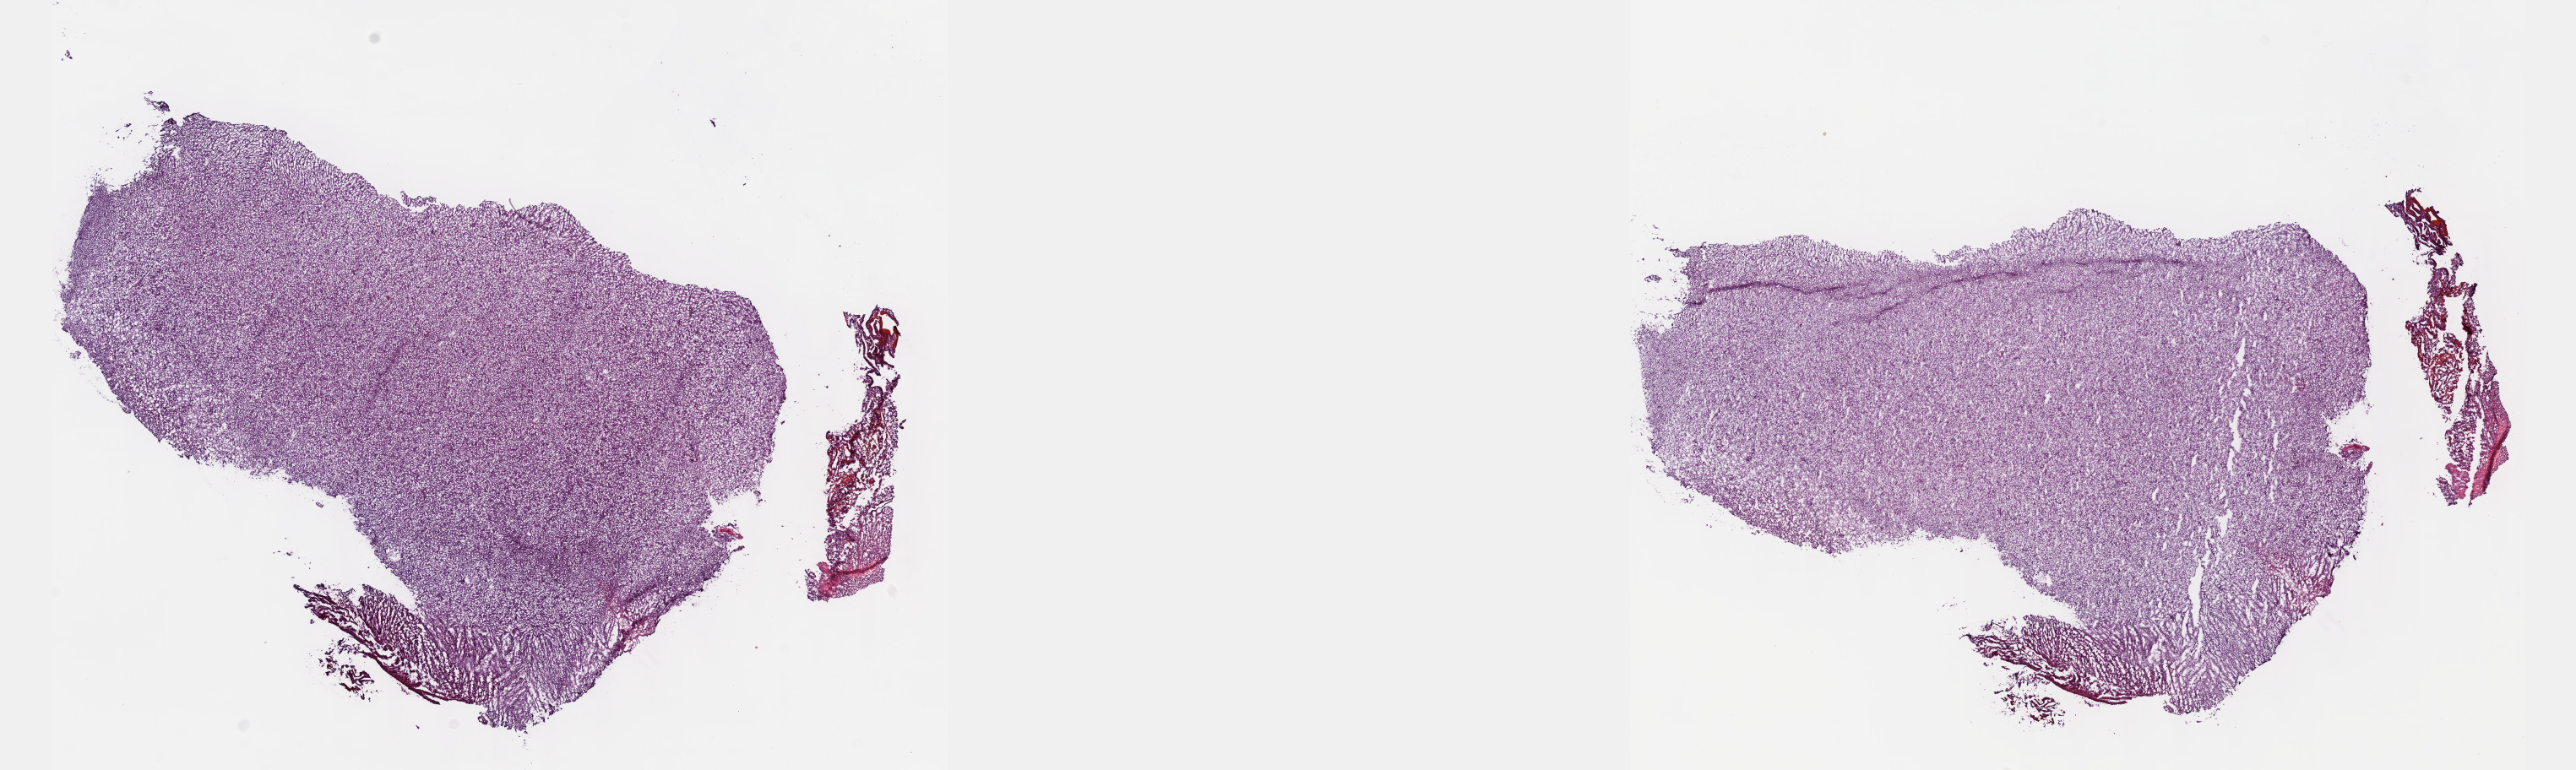
Whole-slide histology image, H&E, a low-resolution overview of the entire scanned area, about 24.6 x 7.4 mm (from a 40x scan). Frozen section. Sample: primary tumour, brain. Patient: female, age at initial diagnosis 58 years. Histologic grade: G2 (moderately differentiated). Composition of this section per pathologist review: tumour cells 30%, tumour nuclei 75%, normal cells 10%, stromal cells 50%, necrosis 10%. Infiltration values recorded for this section: lymphocyte infiltration 0%, monocyte infiltration 0%, neutrophil infiltration 0%.
* diagnosis: Oligodendroglioma, NOS (cerebrum)